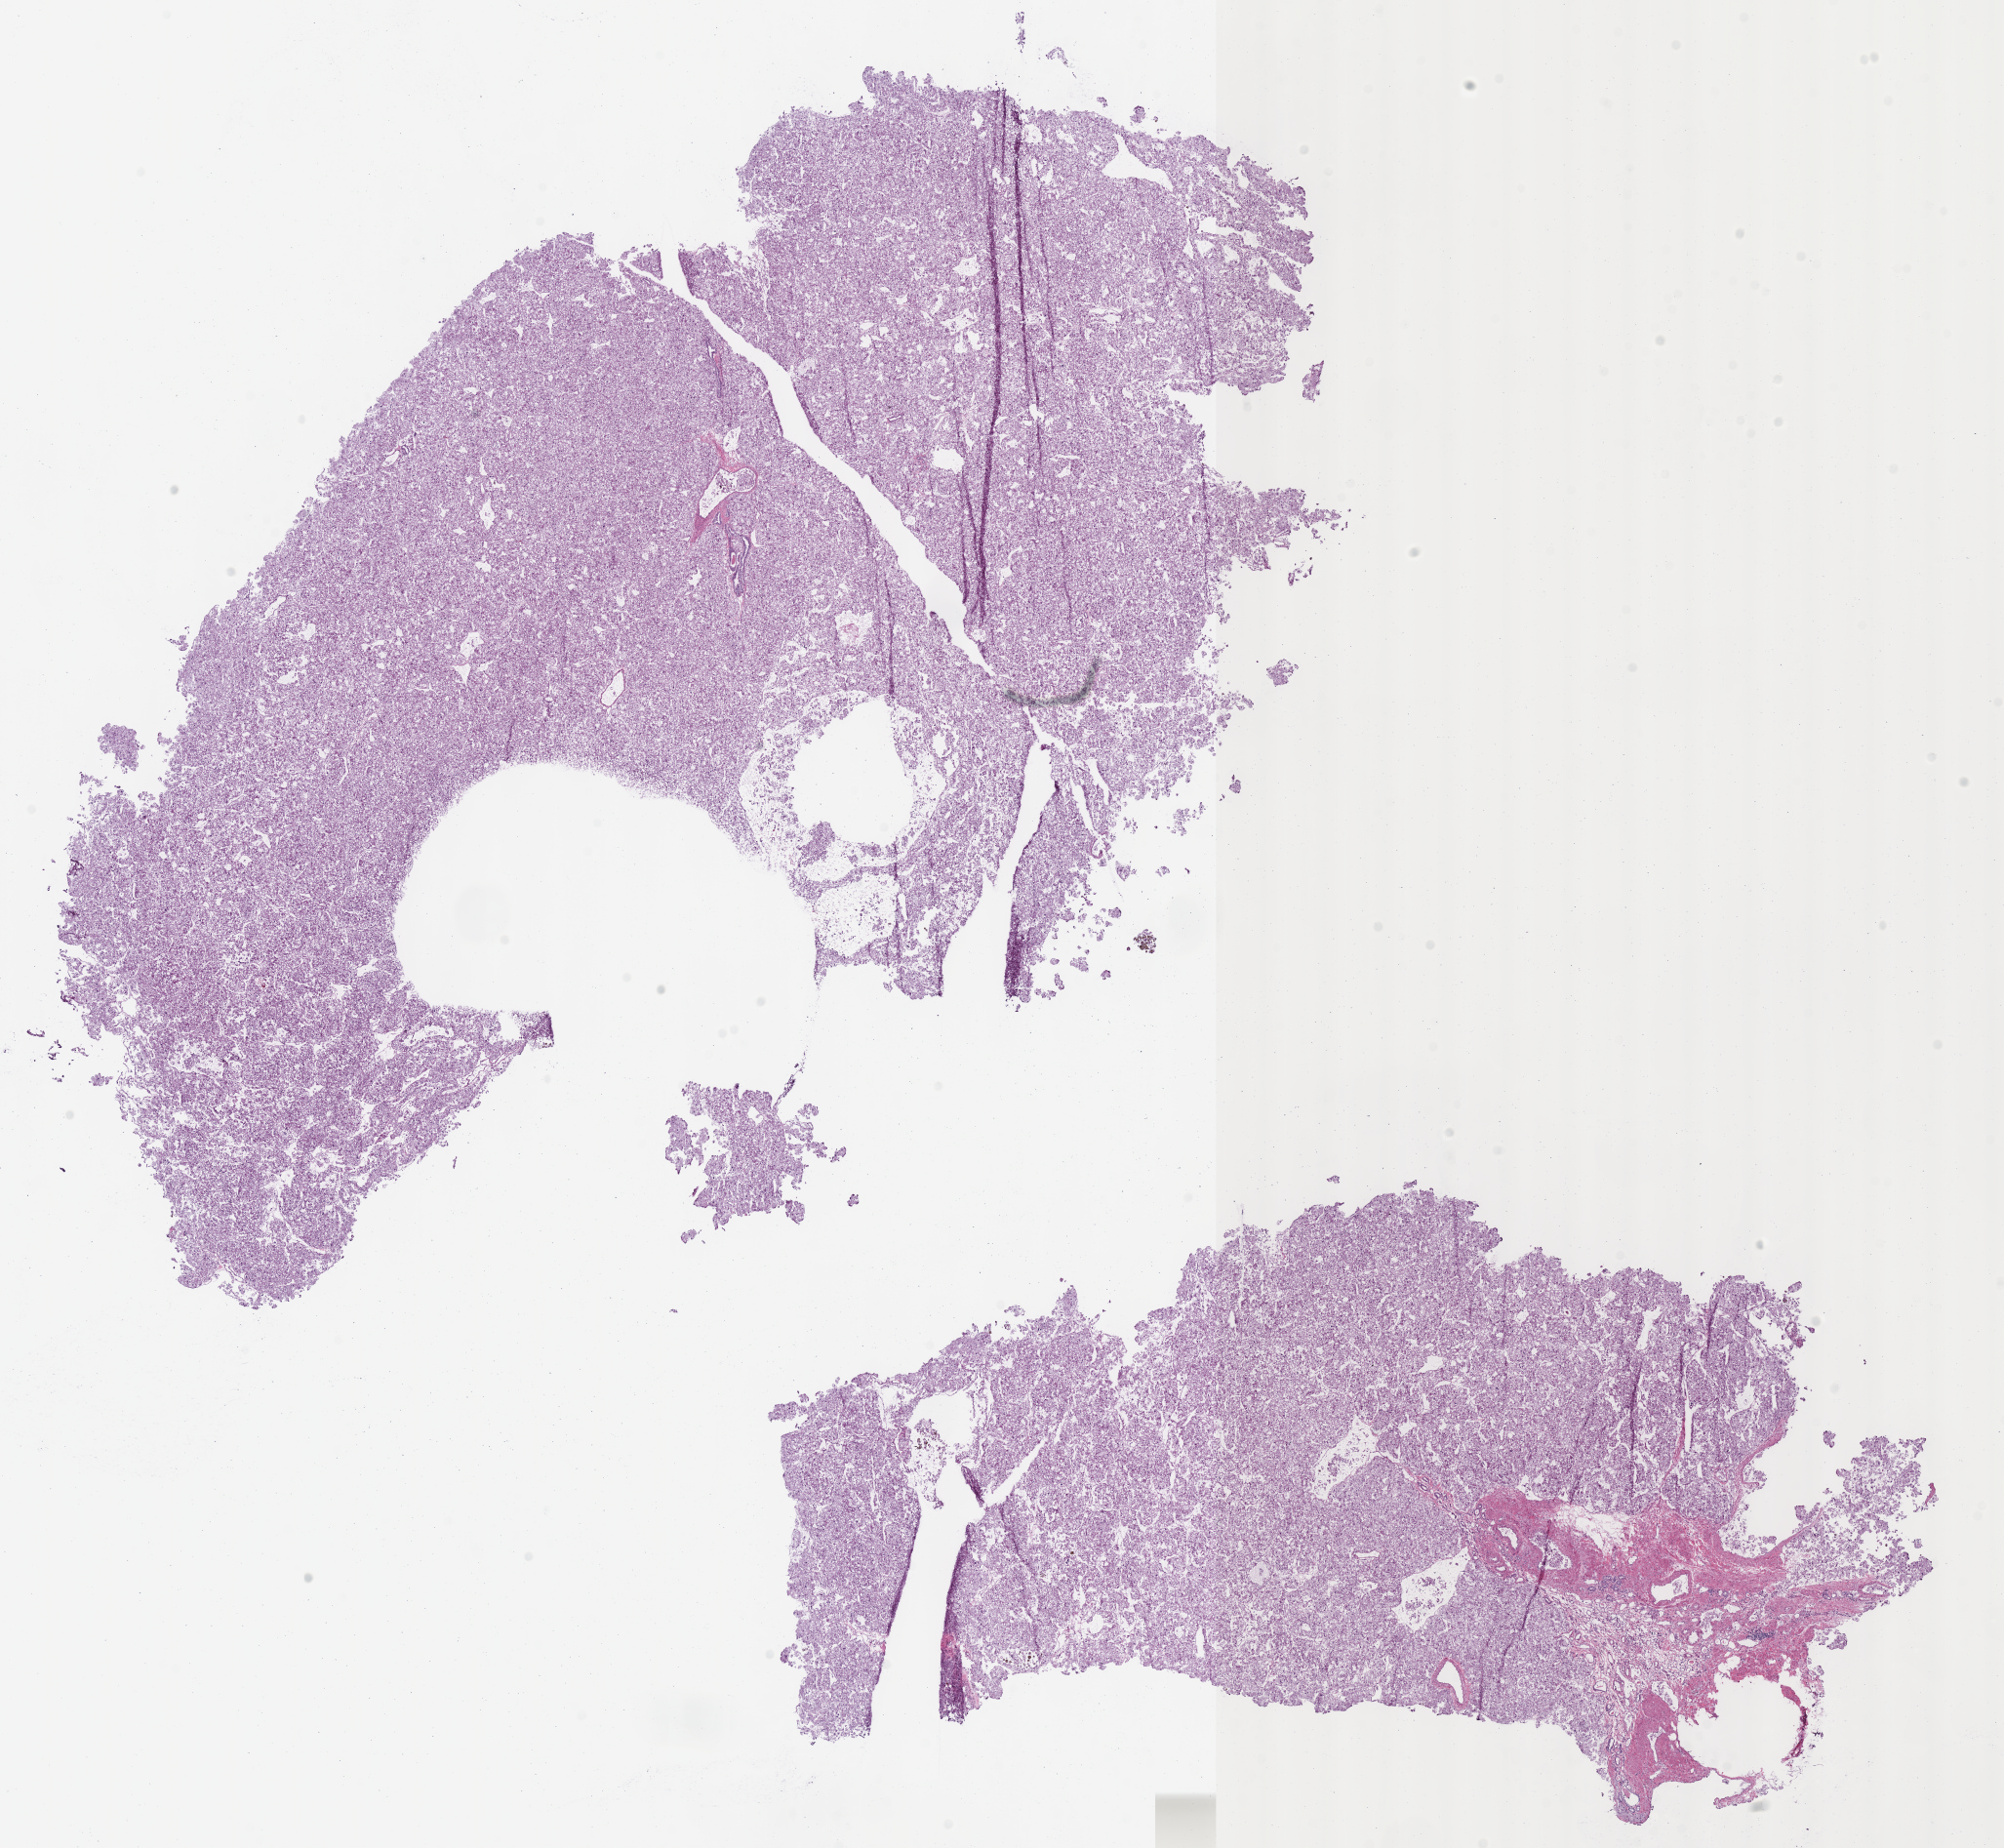
Whole-slide histology image, Hematoxylin and eosin (H&E) stained, shown as a low-resolution overview of the whole scanned area (about 16.2 x 14.9 mm, slide scanned at 40x), frozen section from the bottom of the tissue portion, sample: primary tumour, kidney. Male patient; age at initial diagnosis 72 years. Pathologist review of this section (percent, as recorded): tumour cells 87%, tumour nuclei 90%, normal cells 3%, stromal cells 10%, necrosis 0%.
Pathologic diagnosis: Renal cell carcinoma, chromophobe type. AJCC pathologic stage: III (6th edition). Laterality: right.